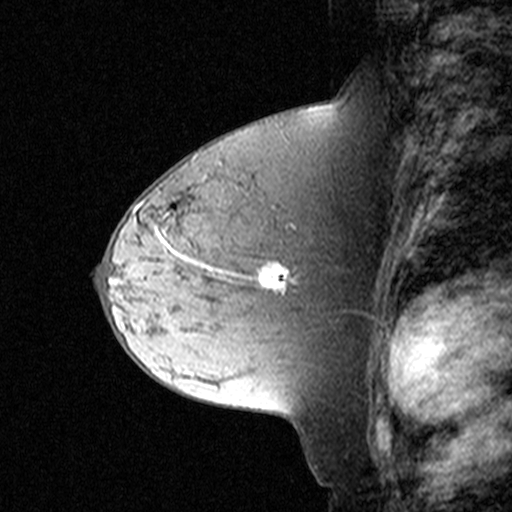
Breast MRI (dynamic contrast-enhanced), one sagittal slice. Slice 20 of 44 in the series (ordered by position). Dynamic contrast-enhanced study with each time point stored as its own series, time point 2 of 3 at this slice position (early post-contrast, ordered by acquisition time). 1.5 T. TE 4.5 ms, TR 11 ms. 3 mm slice thickness. 512 × 512 image matrix, field of view 200 × 200 mm. Female patient, age 44 years. From the clinical record (not read from this slice): setting: breast cancer imaged before/during neoadjuvant chemotherapy; receptor status: triple-negative.
Outlined on this slice (semi-automatically segmented with operator editing):
- analysis volume of interest (the breast-tissue region the enhancement analysis was run in; not a lesion): bounding box <174,204,303,305> (left, top, right, bottom; pixels)
- tumour enhancement mask (voxels above the 90 % enhancement threshold inside the analysis volume of interest): <260,262,289,292>